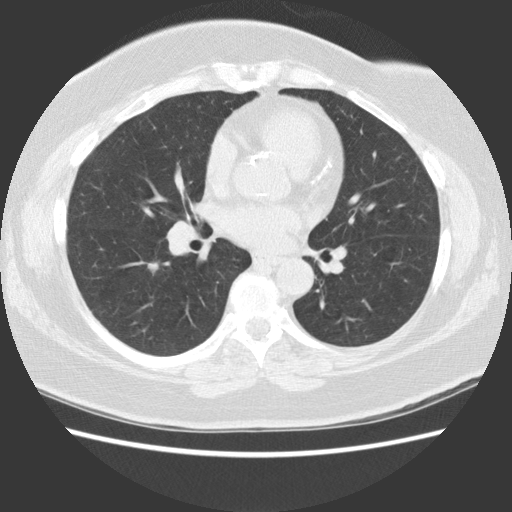
Low-dose screening chest CT, one axial slice. Position 56 of 117 along the scan axis. Reconstruction kernel STANDARD. 140 kVp. Lung window (W 1500 / L -600 HU). 2.5 mm slice thickness. 512 × 512 image matrix, field of view 350 × 350 mm.
Annotated regions visible in this slice (outlined manually by an expert reader):
- lesion 1 (tumor, lower lobe of right lung): bounding box <147,262,159,273> (left, top, right, bottom; pixels)